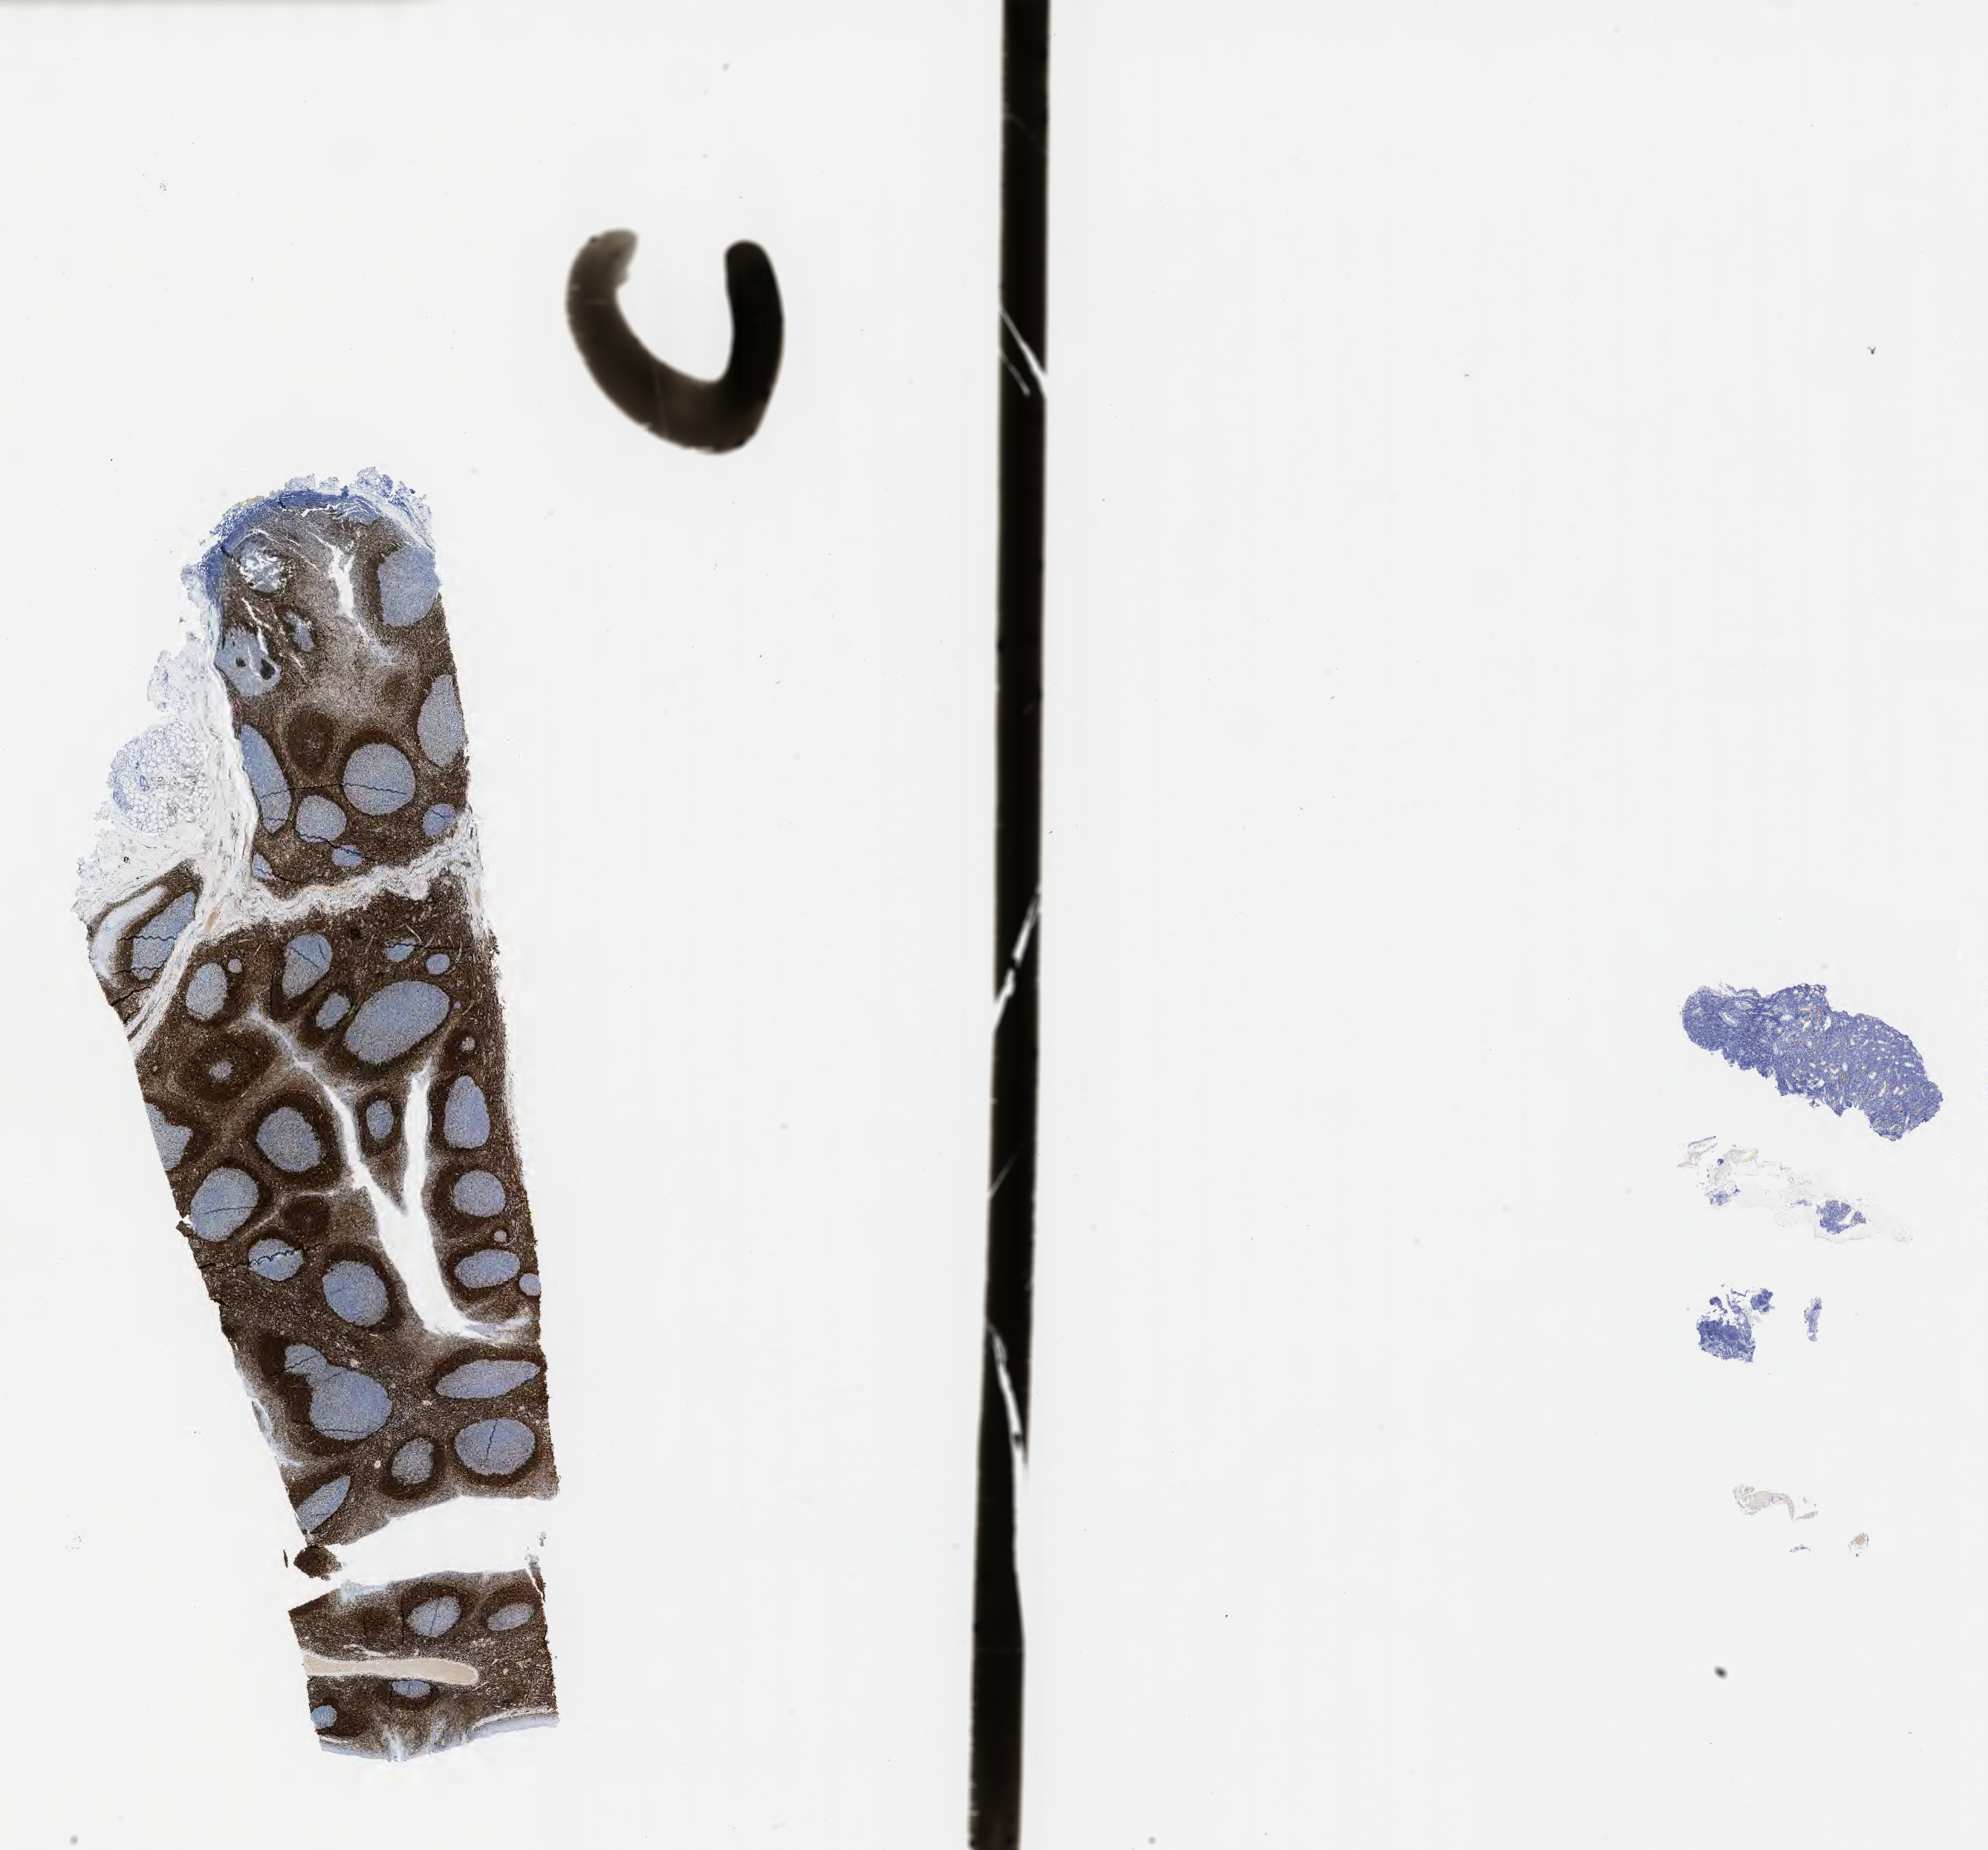
Whole-slide image, immunohistochemical stain for BCL2 — low-resolution overview of the scanned area, about 21.6 x 20.1 mm, tumor tissue, anatomic site: stomach. Female patient, age 28 years.
• histologic diagnosis: Burkitt lymphoma, NOS